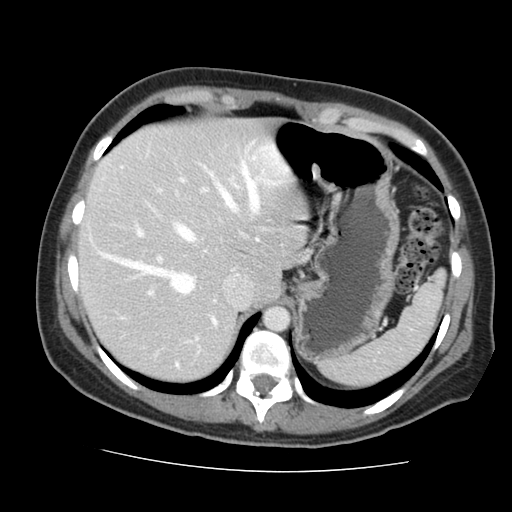
Contrast-enhanced abdominal CT, one axial slice. Position 114 of 144 along the scan axis. 120 kVp. Intravenous contrast given. Soft-tissue window (W 400 / L 40 HU). 512 × 512 image matrix, field of view 333 × 333 mm. Female patient, age 46 years. From the clinical record (not read from this slice): diagnosis: colorectal cancer liver metastases, imaged before liver resection; multiple liver metastases: no; largest metastasis: 2.8 cm; disease in both lobes: no.
Annotated regions visible in this slice (expert manual segmentation):
- hepatic veins: bounding box <102,162,259,294> (left, top, right, bottom; pixels)
- liver: <80,120,303,380>
- planned liver remnant (the part of the liver to remain after resection): <80,120,303,380>
- portal vein (with intrahepatic branches): <136,176,239,367>